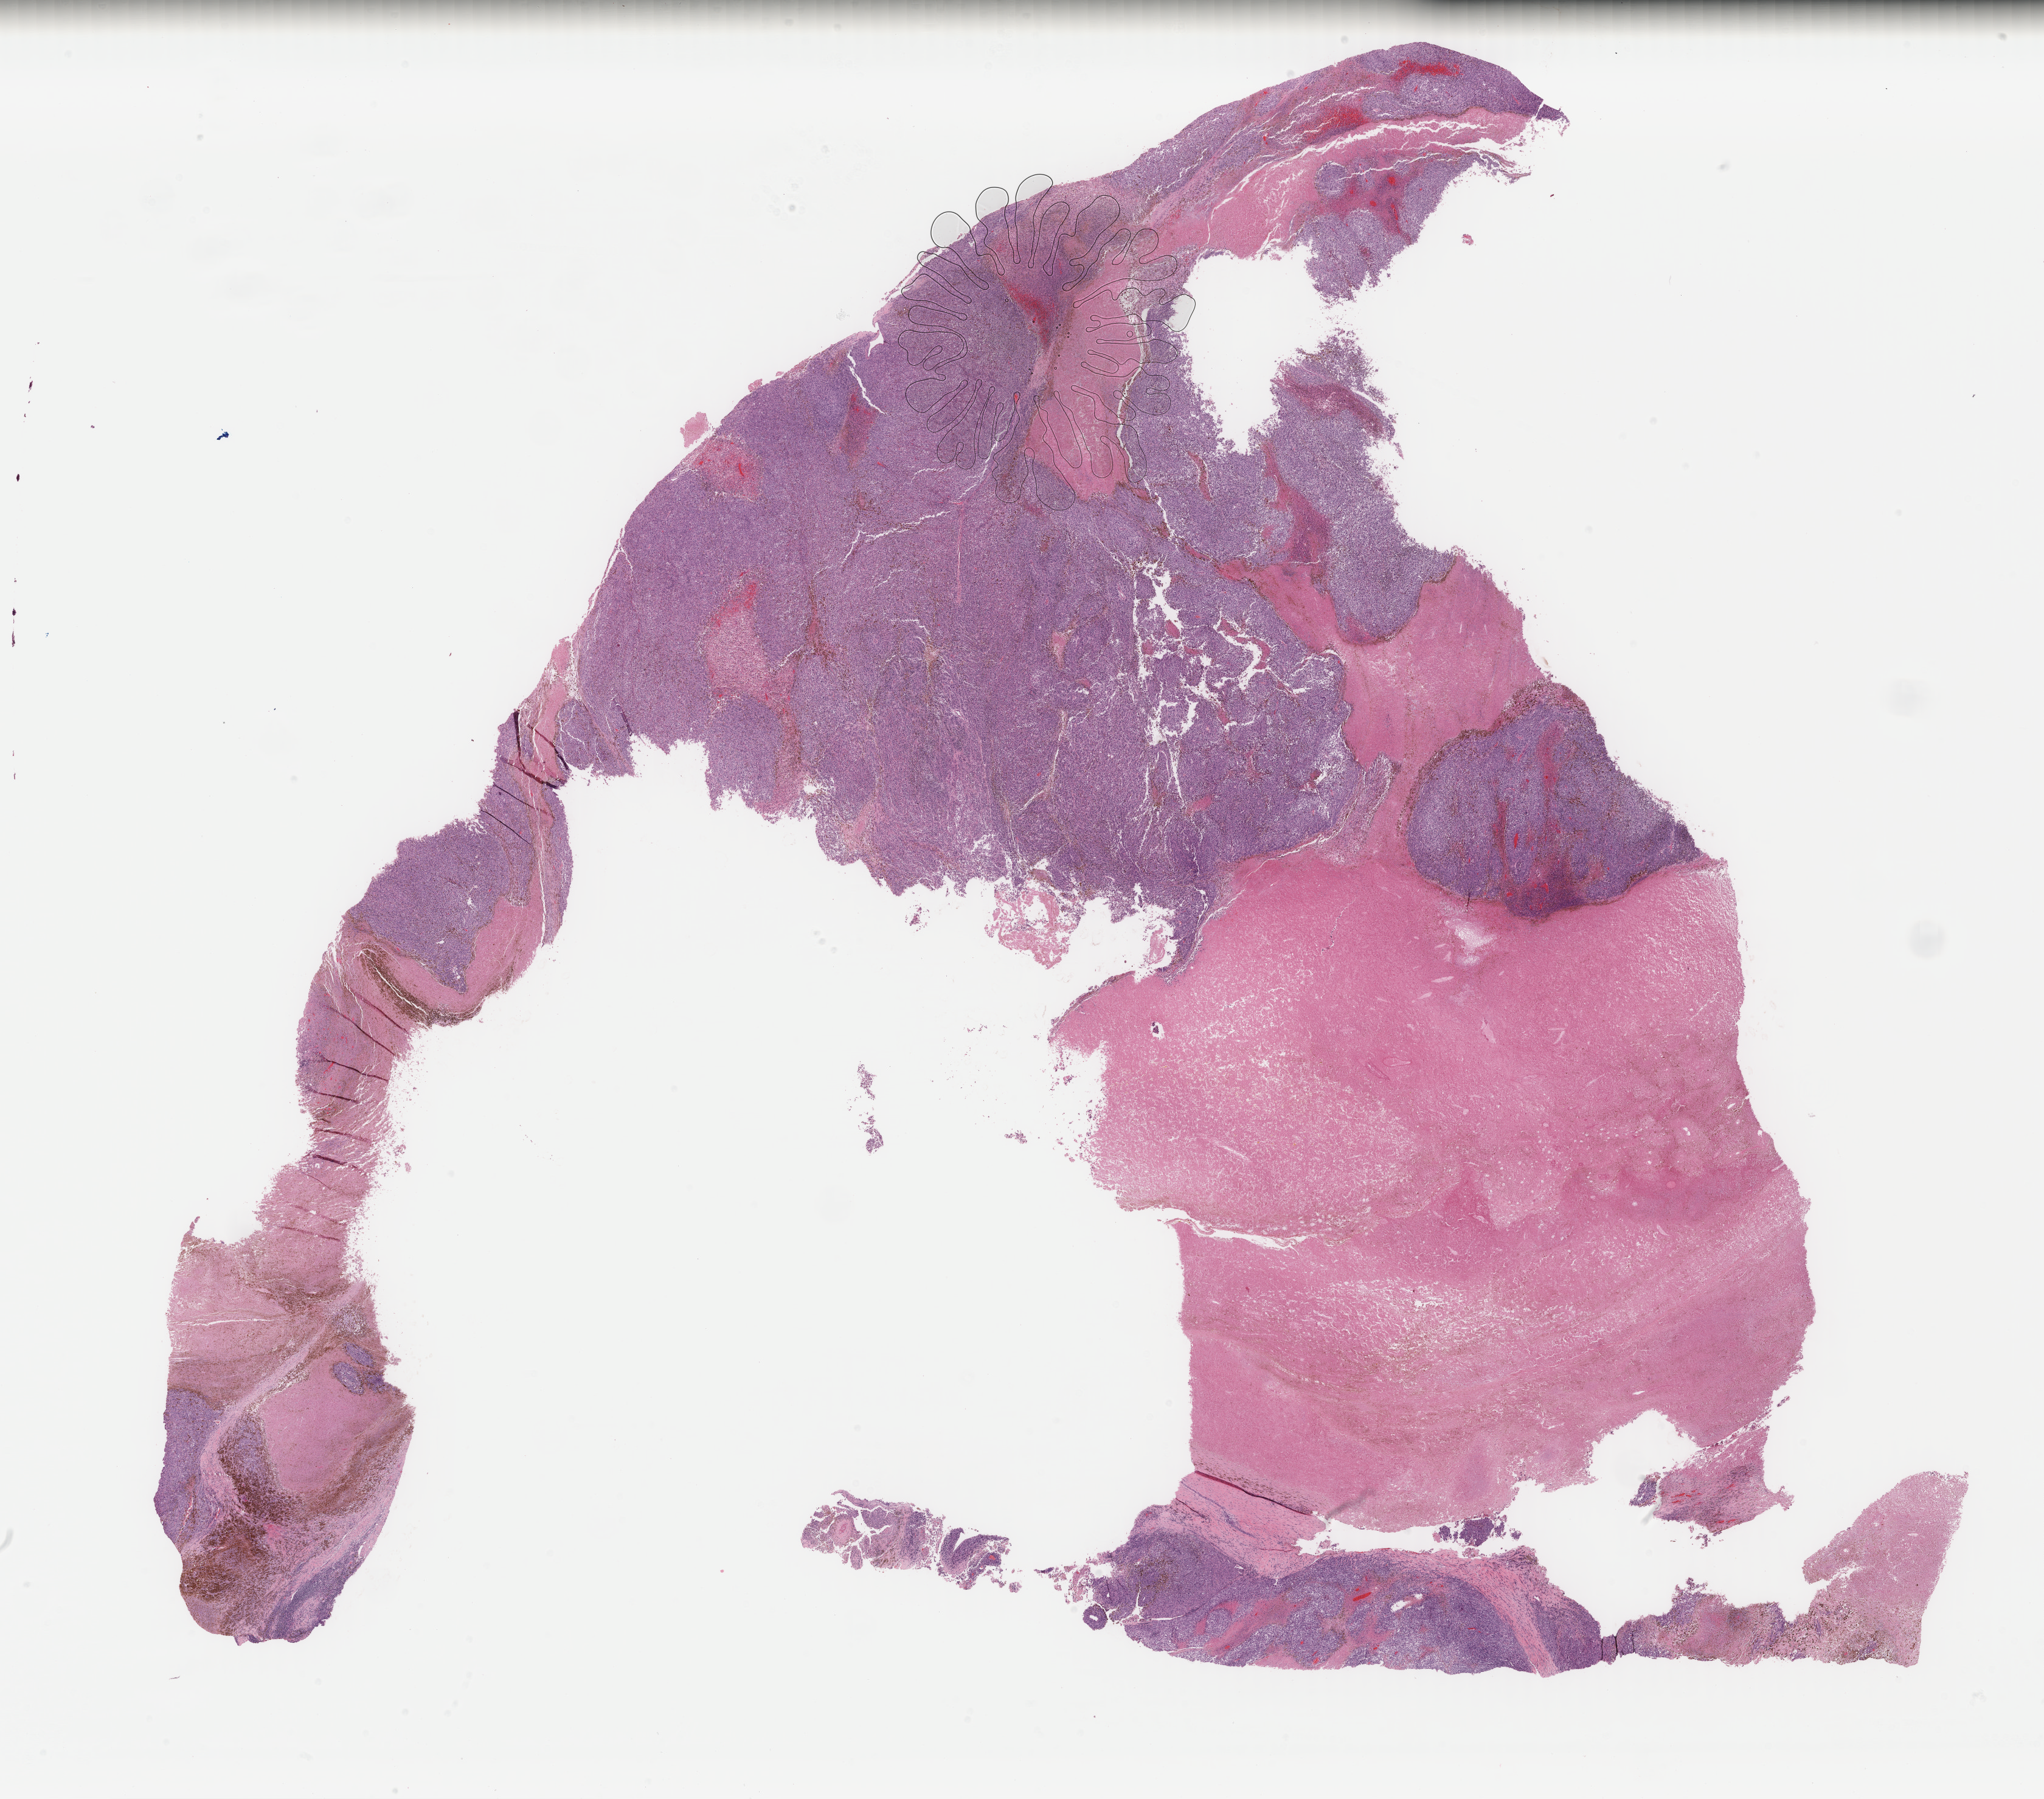
Hematoxylin and eosin (H&E) stained whole-slide image — low-resolution overview of the scanned area, about 26.7 x 23.5 mm (acquisition: 40x scan); formalin-fixed paraffin-embedded (FFPE) diagnostic section; skin, primary tumour sample. Patient: female, age at initial diagnosis 37 years.
Diagnosis: Malignant melanoma, NOS.